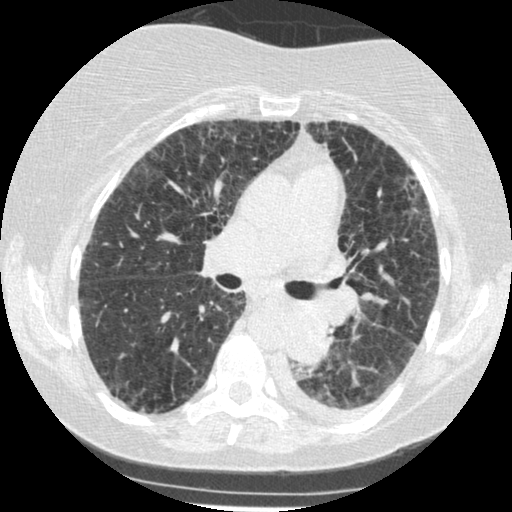
Low-dose screening chest CT, axial slice; third annual screen; lung window (W 1500 / L -600 HU); 1.25 mm slice thickness; standard (soft-tissue) reconstruction kernel (STANDARD). Female, age 60 years at enrolment. Former smoker at enrolment.
- Expert reader's lesion annotation, bounding box <270,308,342,374> (left, top, right, bottom; pixels).
- Reader record for this screening exam (exam-level; its link to the box is not recorded): non-calcified nodule or mass ≥4 mm, left lower lobe, 54 × 38 mm, smooth margins, soft tissue attenuation, pre-existing on the prior screen: yes; interval growth: yes.
- Official screen result: positive, other.
- Lung cancer was diagnosed 15 days after this screen: small cell carcinoma, NOS, left lower lobe, undifferentiated (G4), stage IV (AJCC 6th edition), 69 mm at pathology.